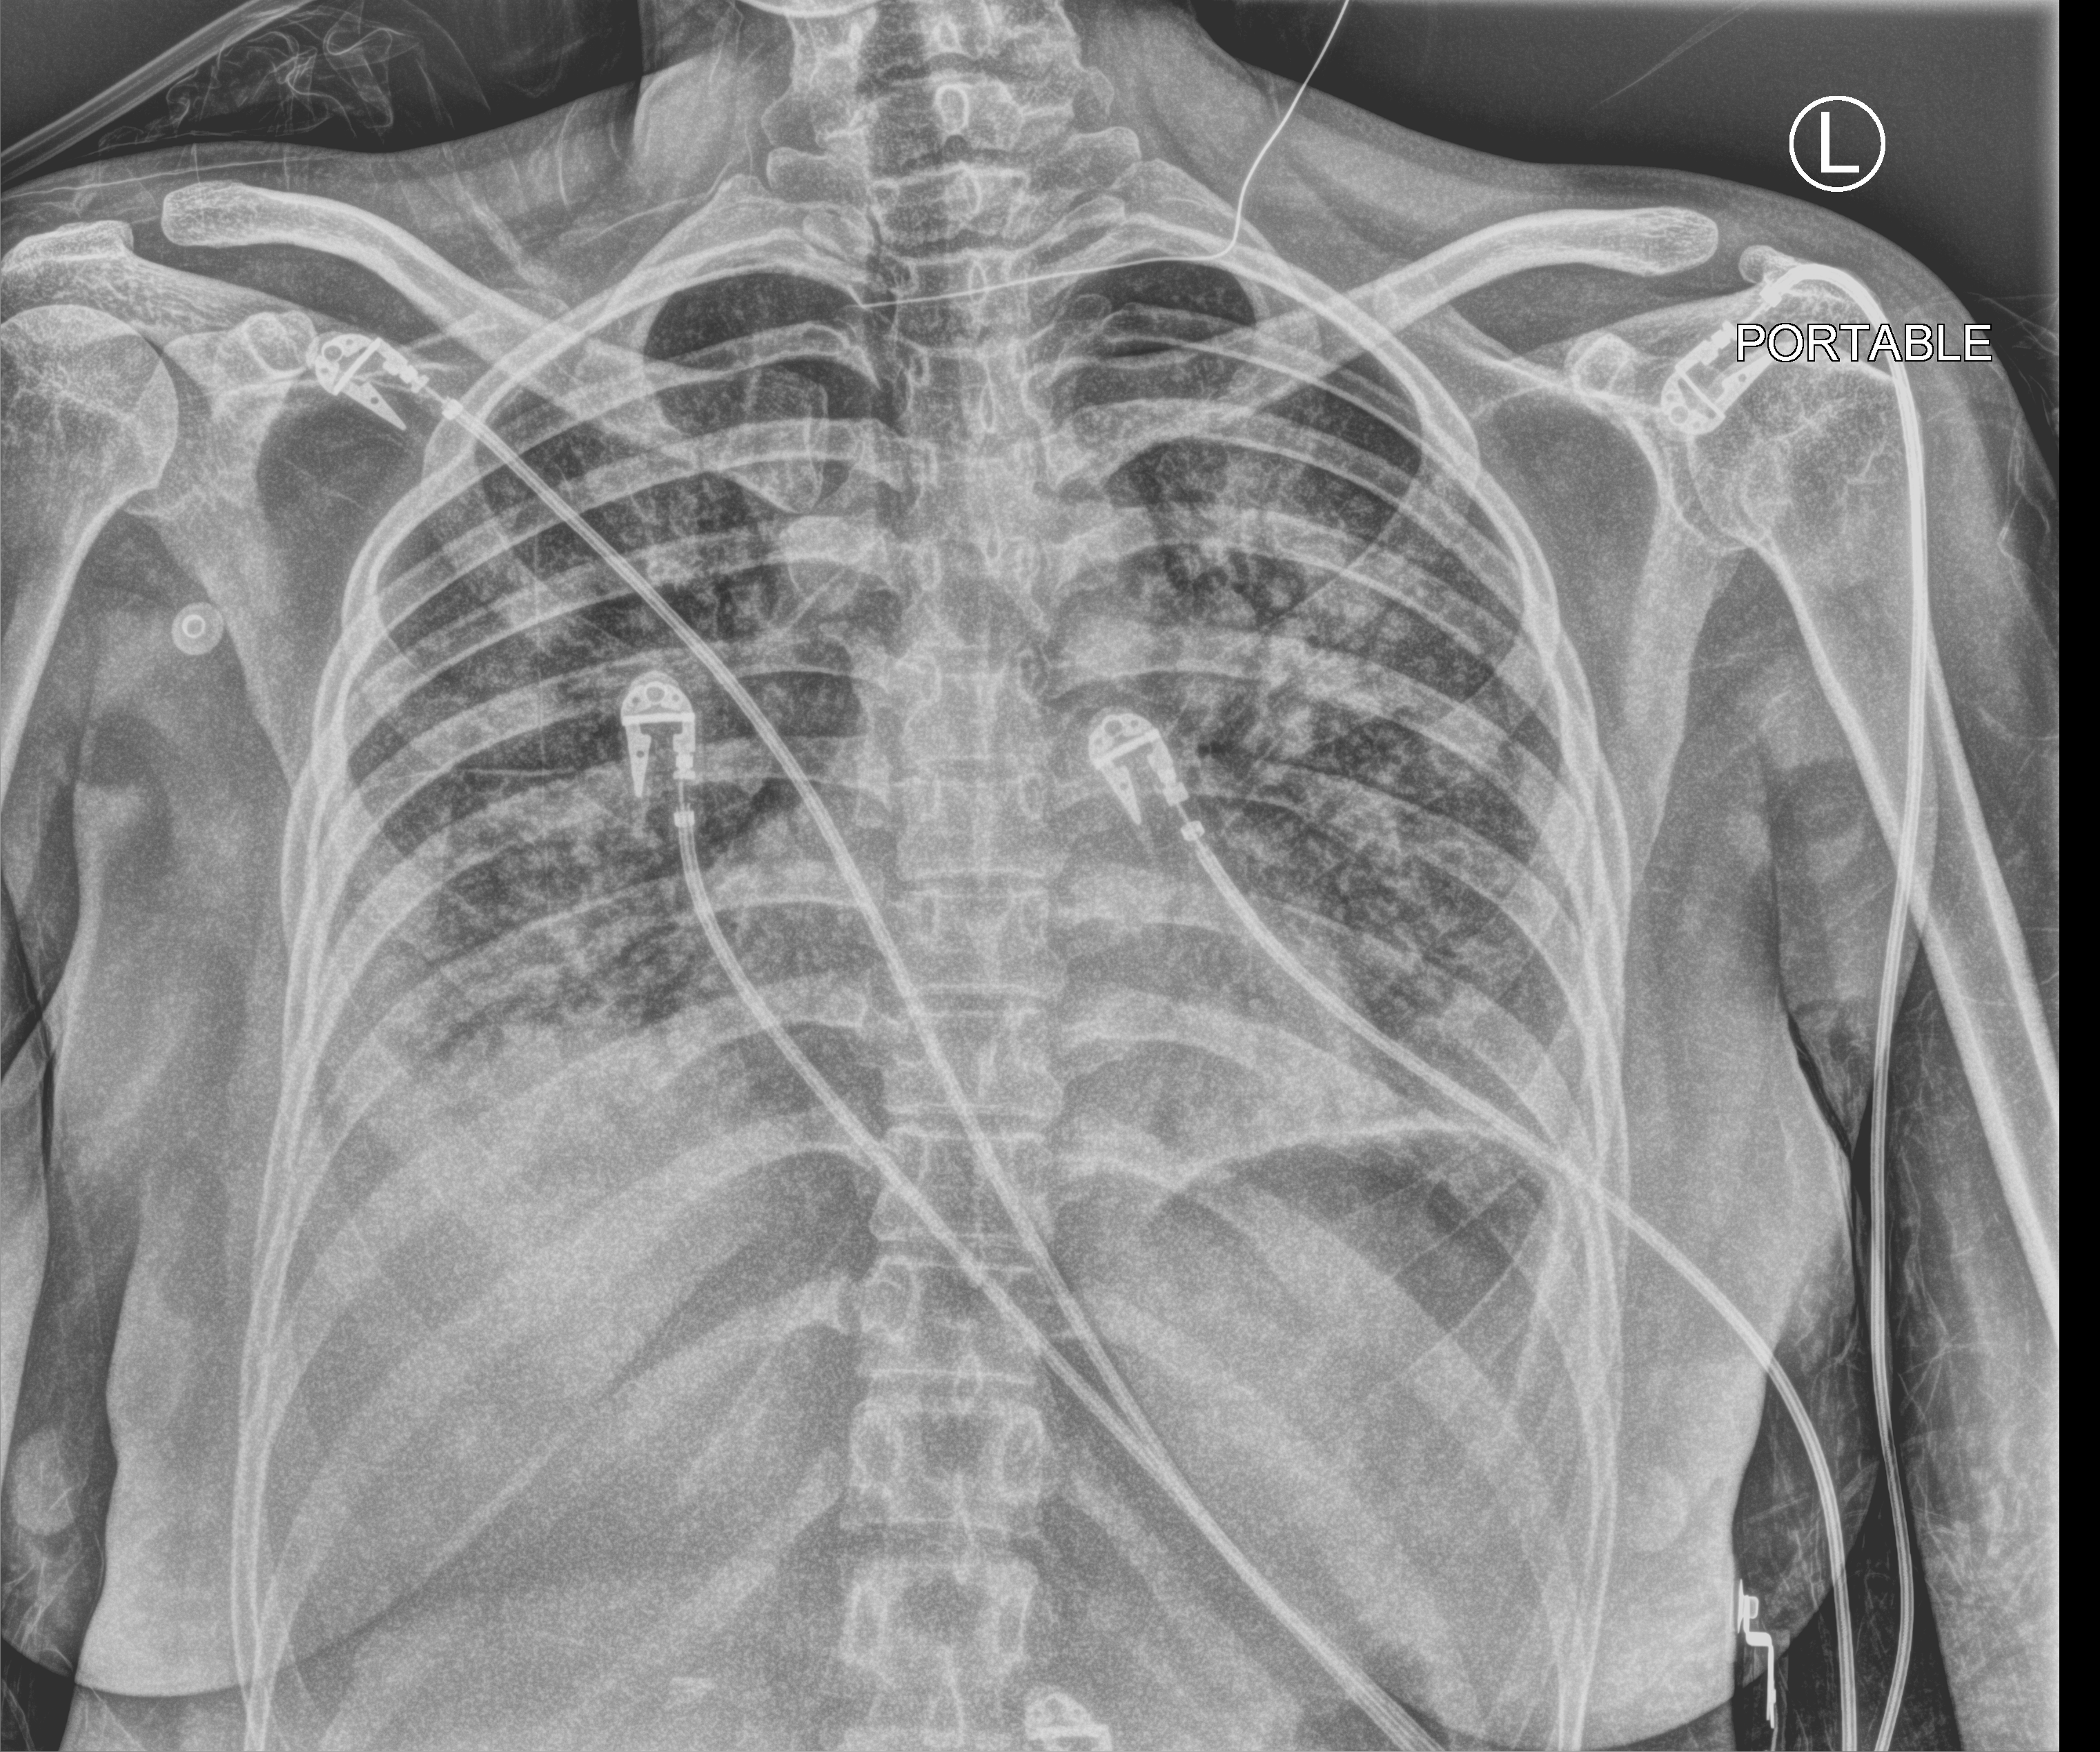
Bedside chest radiograph (computed radiography); anteroposterior (AP) projection. Adult patient hospitalised with COVID-19, age 18–59 years.
Hospital-stay facts (about this admission, not read from this image; timing relative to this image not recorded): diabetes (admission record): no; mechanically ventilated during this hospital stay: yes.